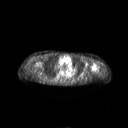
FDG PET of an extremity soft-tissue mass (from a PET/CT study), one axial slice; slice 187 of 267 in the series (ordered by position); 3.27 mm slice thickness; 128 × 128 image matrix. Female patient, age 83 years. From the clinical record (not read from this slice): histological type: pleiomorphic leiomyosarcoma; grade: high; site of the primary tumour: left biceps.
Outlined on this slice (expert contour drawn on MRI and transferred to this co-registered scan by the dataset authors):
- gross tumour volume including surrounding oedema: box from (x=91, y=64) to (x=97, y=72) px